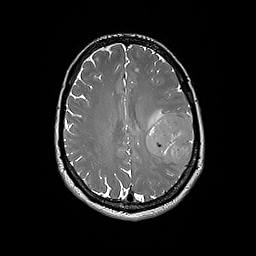
Brain MRI from a brain-tumour surgery series, one axial slice; position 76 of 192 along the scan axis; 1 mm slice thickness; 256 × 256 image matrix. Case-level facts recorded for this patient, not image findings: histopathology: Glioblastoma; WHO grade: 4; IDH mutation: no; tumour location: Left Frontal.
Structures marked on this image (expert manual segmentation):
- tumour: bounding box <146,113,195,165> (left, top, right, bottom; pixels)